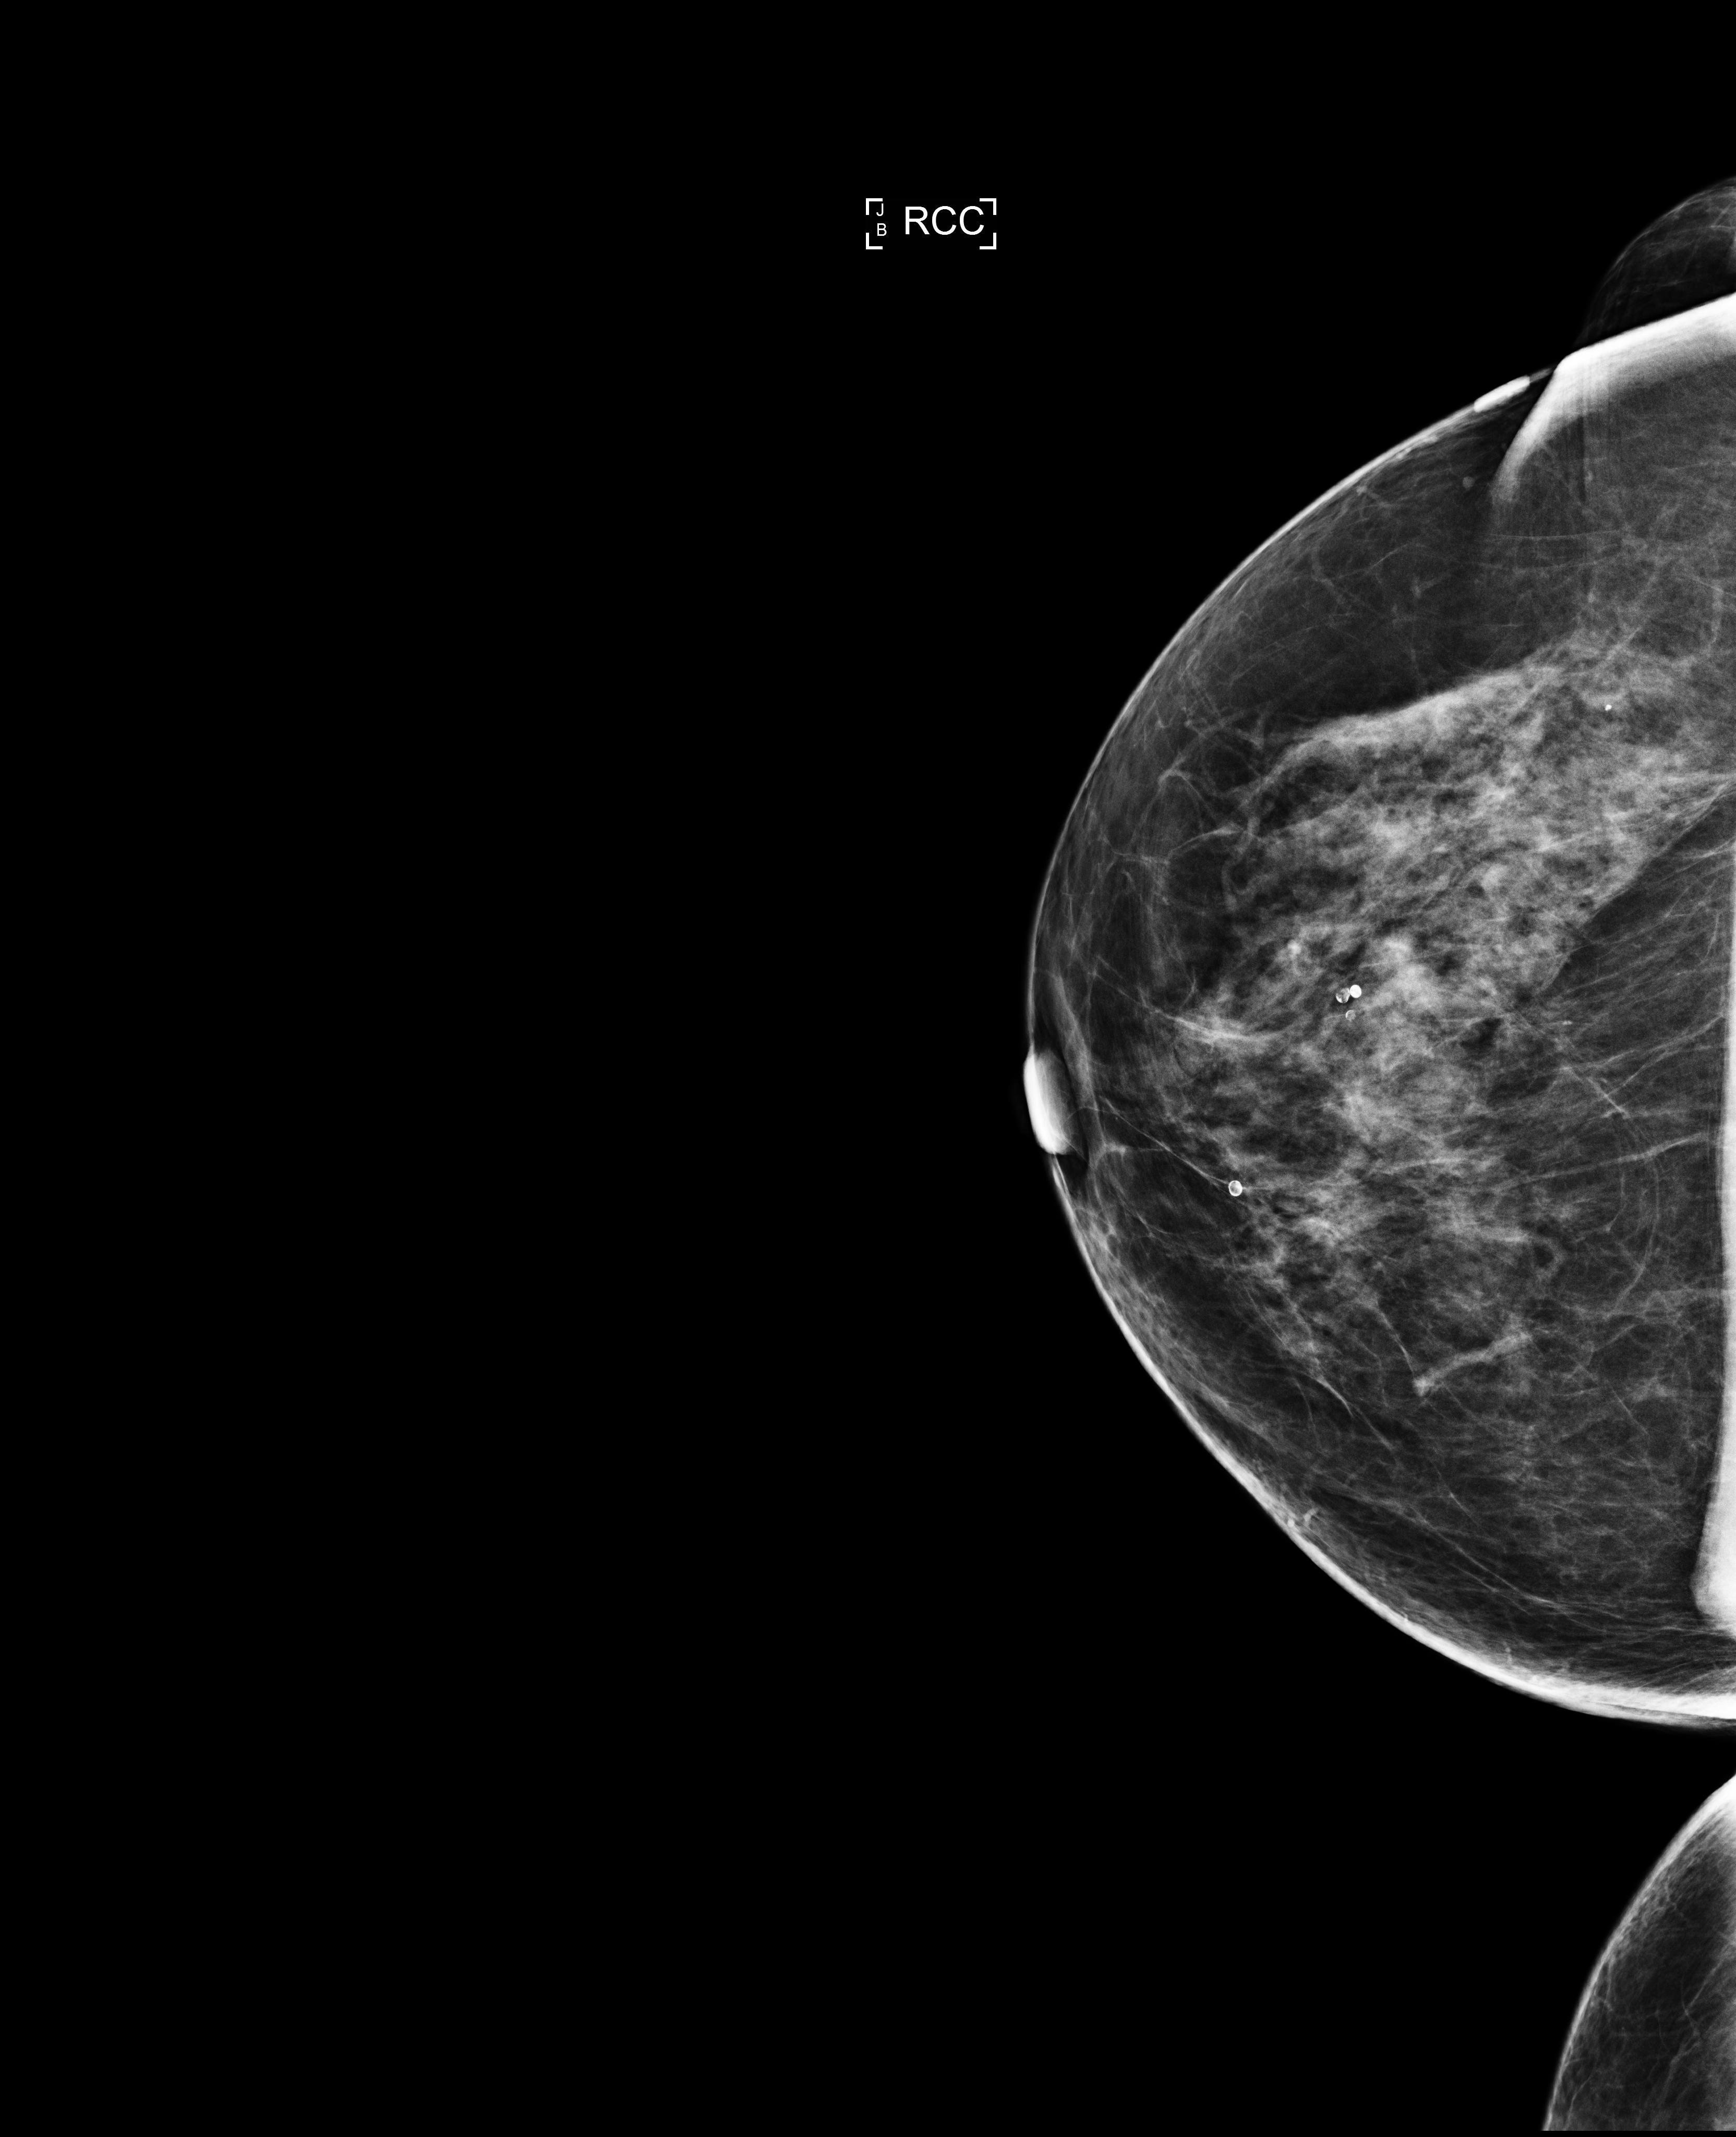
Full-field digital mammogram (FFDM); right breast; craniocaudal (CC) view; screening examination; compressed breast thickness 62 mm; system: Selenia Dimensions. Female patient, age 63 years.
- breast density at the screening exam (both breasts): scattered fibroglandular densities (BI-RADS density category b)
- final BI-RADS category for the screening round (tomosynthesis exam, both breasts): category 1
- recall: no recall after this screen